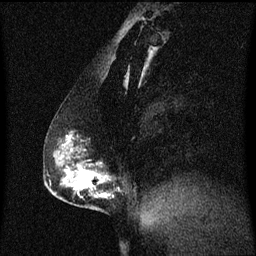
Breast MRI (dynamic contrast-enhanced), one sagittal slice. Slice 30 of 60 in the series (ordered by position). Dynamic contrast-enhanced series, image 2 of 3 at this slice position (ordered by acquisition). 1.5 T. TE 4.2 ms, TR 8.4 ms. 2 mm slice thickness. 256 × 256 image matrix, field of view 200 × 200 mm. Patient: female, 40 years. Case-level facts recorded for this patient, not image findings: setting: breast cancer imaged before/during neoadjuvant chemotherapy; receptor status: triple-negative.
Annotated regions visible in this slice (semi-automatic segmentation, software-assisted and operator-edited):
- analysis volume of interest (the breast-tissue region the enhancement analysis was run in; not a lesion): bounding box [x1, y1, x2, y2] px = [58, 132, 117, 211]
- tumour enhancement mask (voxels above the 70 % enhancement threshold inside the analysis volume of interest): [66, 136, 111, 199]